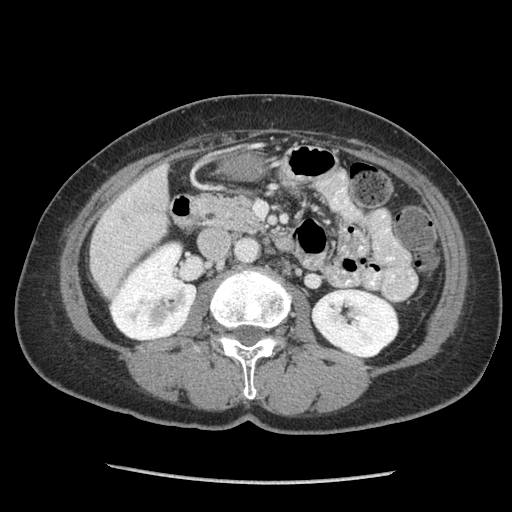
Contrast-enhanced abdominal CT (liver protocol), one axial slice; slice 25 of 105 in the series (ordered by position); reconstruction kernel STANDARD; soft-tissue window (W 400 / L 40 HU); 2.5 mm slice thickness; 512 × 512 image matrix, field of view 340 × 340 mm. Case-level facts recorded for this patient, not image findings: diagnosis: hepatocellular carcinoma (patient treated with transarterial chemoembolisation; whether this scan precedes or follows treatment is not stated here); TNM stage (as recorded): Stage-I; Child-Pugh class: A; tumour differentiation: moderately differentiated; tumour size: 11.1 cm.
Outlined on this slice (semi-automatically segmented with operator editing):
- liver parenchyma outside the tumour (the mass and vessels are separate outlines, so this box may not span the whole liver): box from (x=90, y=164) to (x=168, y=296) px
- liver vessels: (x=110, y=186)–(x=146, y=247)